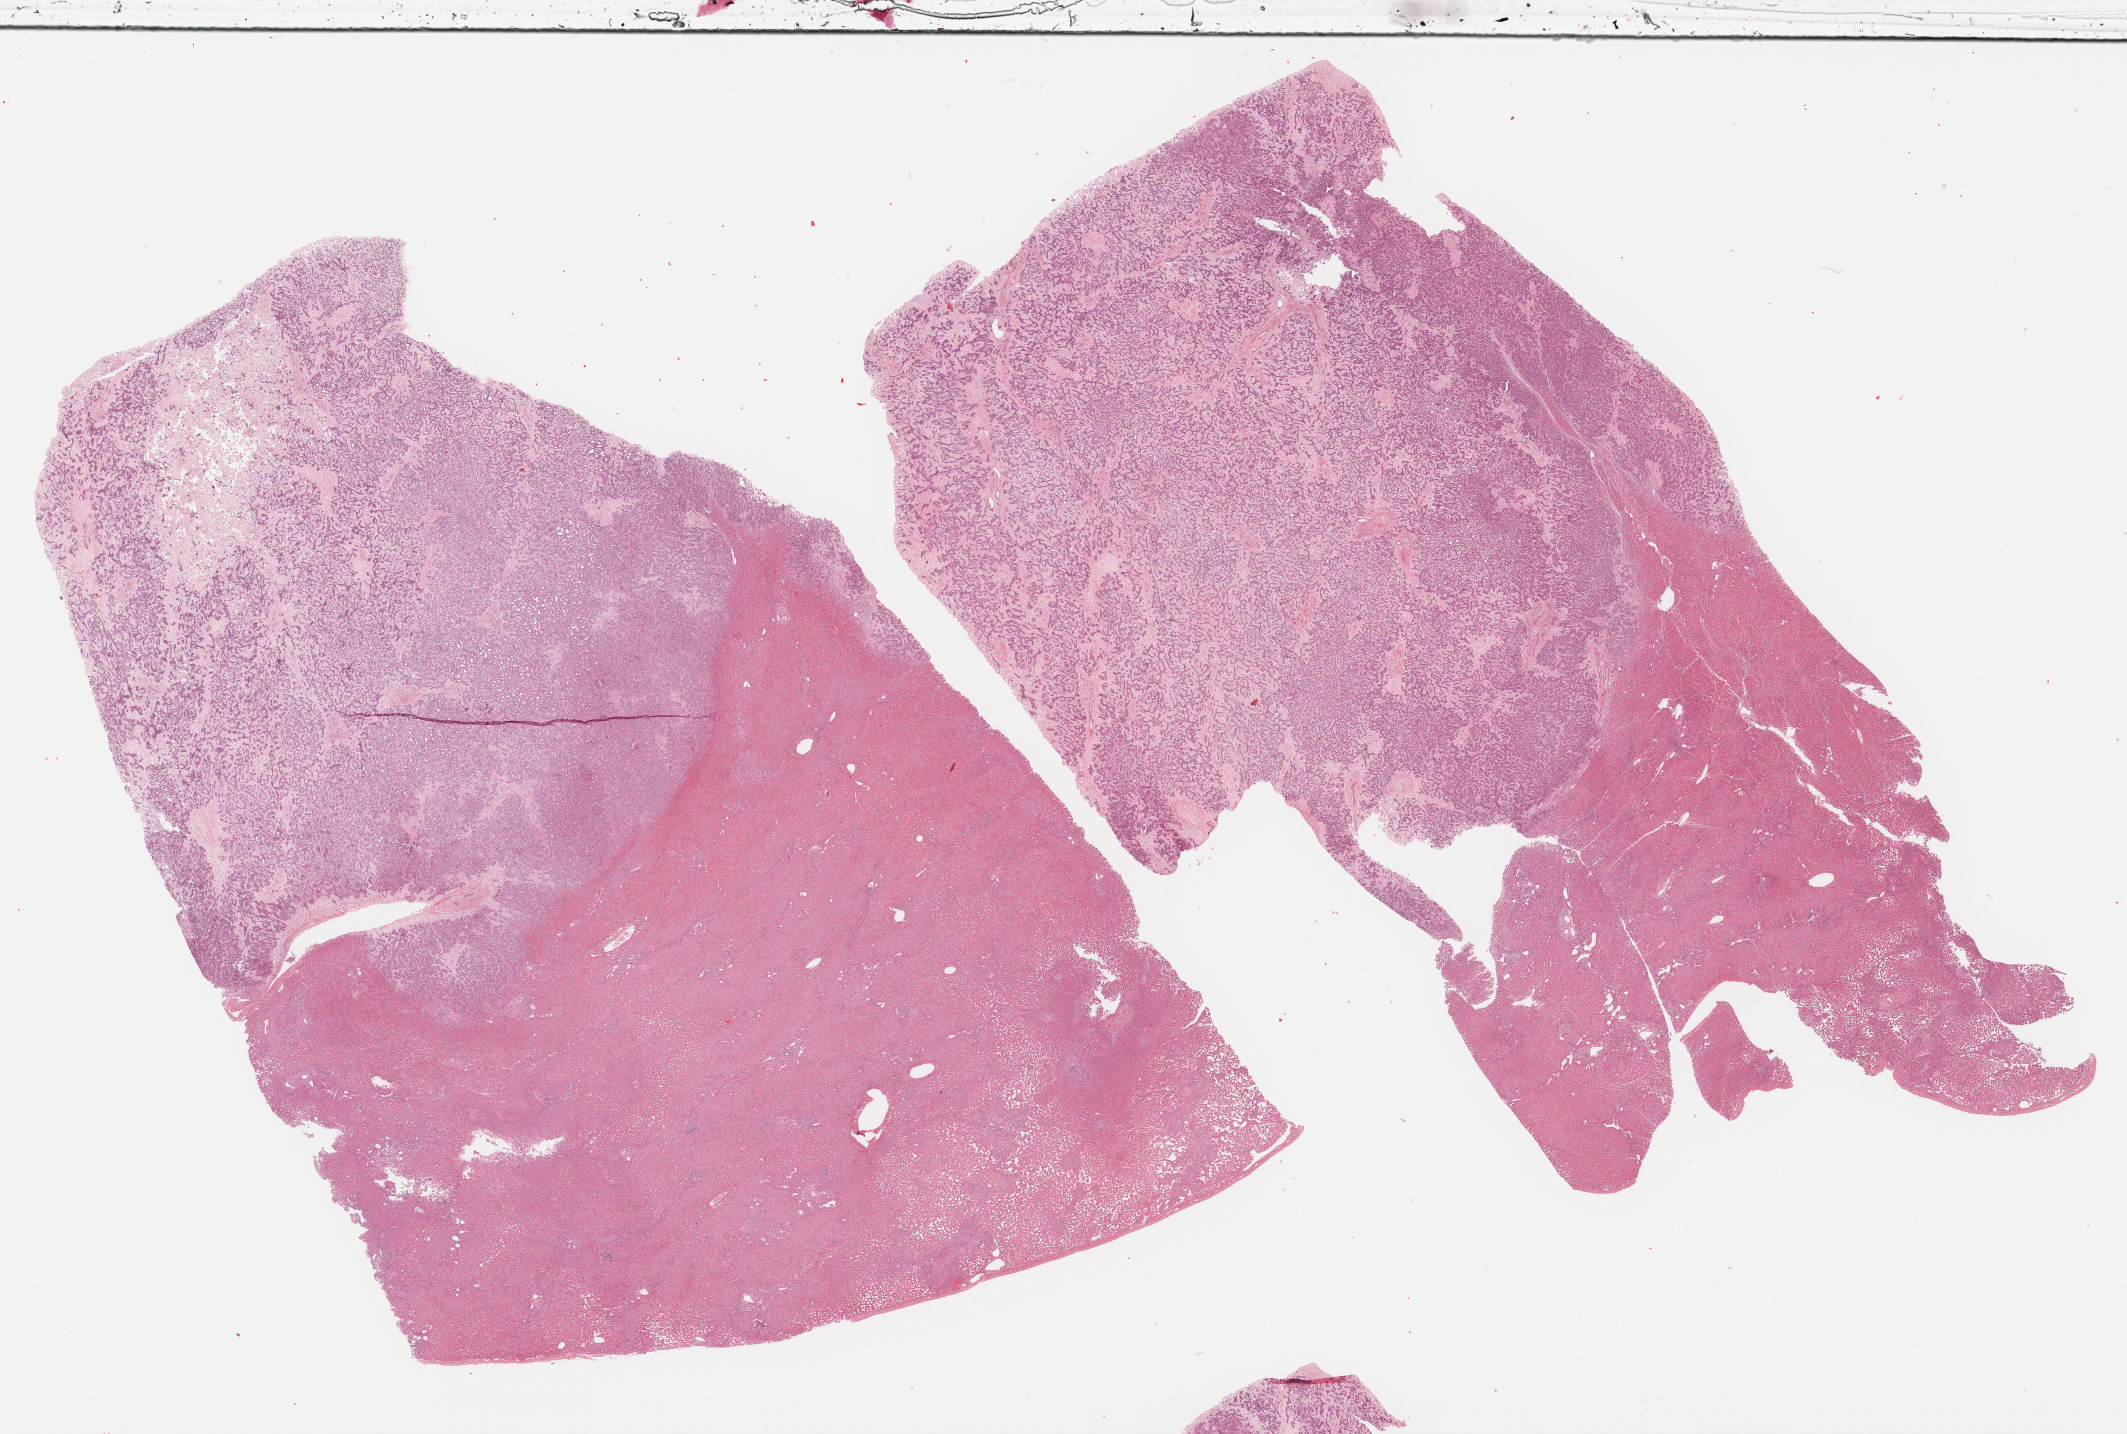
Whole-slide histology image, H&E-stained, a low-resolution overview of the entire scanned area, about 34.4 x 23.2 mm (from a 40x scan). Formalin-fixed paraffin-embedded (FFPE) diagnostic section. Bile duct, primary tumour sample. Female patient; age at initial diagnosis 29 years. Histologic grade: G3 (poorly differentiated).
• TNM: T2 N0 M0
• pathologic diagnosis: Cholangiocarcinoma (intrahepatic bile duct)
• AJCC pathologic stage: II (7th edition)